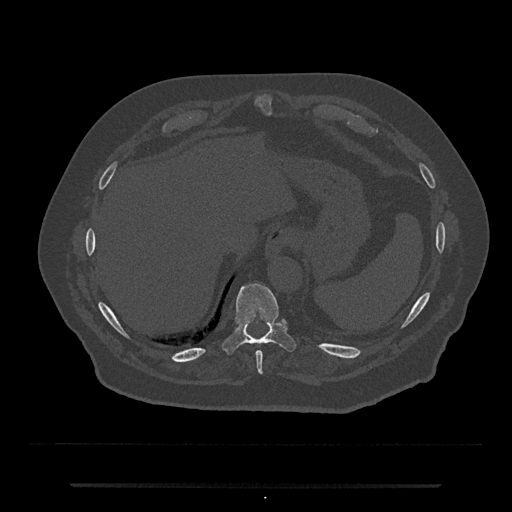
CT including the spine, one axial slice. Reconstruction kernel Br40s/3. Bone window (W 1800 / L 400 HU). 0.5 mm slice thickness. 512 × 512 image matrix, field of view 434 × 434 mm. Patient: male, 80 years. From the clinical record (not read from this slice): primary cancer: prostate; vertebrae with lytic lesions (as recorded): L1, T11.
Outlined on this slice (semi-automatically segmented with operator editing):
- T10 vertebra: bounding box (x1, y1, x2, y2) in pixels: (222, 283, 295, 354)
- T9 vertebra: (256, 351, 263, 374)